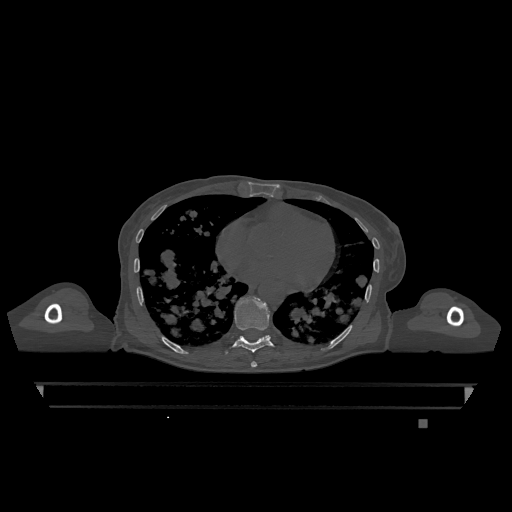
CT including the spine, one axial slice; slice 686 of 1317 in the series (ordered by position); bone window (W 1800 / L 400 HU); 0.5 mm slice thickness; 512 × 512 image matrix. Patient: female, 74 years. From the clinical record (not read from this slice): primary cancer: lung; vertebrae with lytic lesions (as recorded): T1, T4, T5, T6, L4, L5.
Annotated regions visible in this slice (semi-automatically segmented with operator editing):
- T10 vertebra: box from (x=265, y=336) to (x=269, y=337) px
- T7 vertebra: (x=251, y=361)–(x=257, y=368)
- T9 vertebra: (x=225, y=297)–(x=274, y=354)